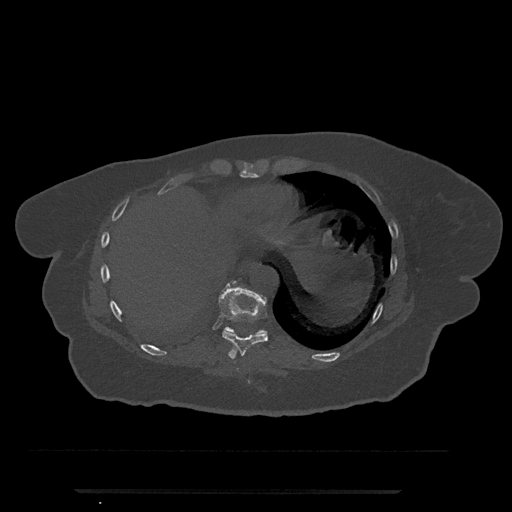
CT including the spine, one axial slice. Position 327 of 797 along the scan axis. Reconstruction kernel Br40s/3. 120 kVp. Bone window (W 1800 / L 400 HU). 0.5 mm slice thickness. 512 × 512 image matrix. Female patient, age 51 years. From the clinical record (not read from this slice): primary cancer: neuro; vertebrae with lytic lesions (as recorded): T8.
Structures marked on this image (semi-automatically segmented with operator editing):
- T10 vertebra: bounding box [x1, y1, x2, y2] px = [224, 327, 265, 335]
- T8 vertebra: [237, 368, 239, 371]
- T9 vertebra: [219, 281, 268, 359]